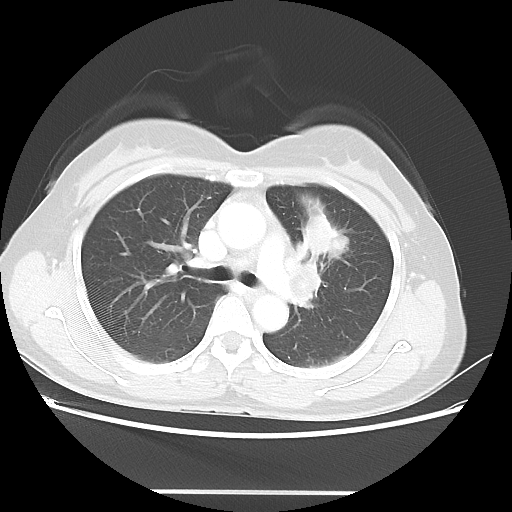
Chest CT, one axial slice. Reconstruction kernel LUNG. 100 kVp. Lung window (W 1500 / L -600 HU). 512 × 512 image matrix, field of view 360 × 360 mm. Patient: female, 50 years. Case-level facts recorded for this patient, not image findings: clinical TNM (as recorded): T1c N1 M0; histopathological grade: G3.
Outlined on this slice (bounding box drawn by a radiologist):
- lung tumour (recorded histology: adenocarcinoma): bounding box (x1, y1, x2, y2) in pixels: (299, 212, 349, 256)